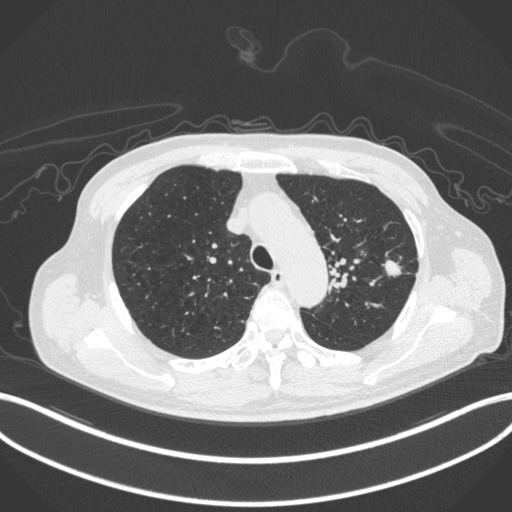
Chest CT, one axial slice; position 334 of 420 along the scan axis; reconstruction kernel B31f; 120 kVp; lung window (W 1500 / L -600 HU); 1 mm slice thickness; 512 × 512 image matrix, field of view 400 × 400 mm. Patient: male, 77 years. From the clinical record (not read from this slice): clinical TNM (as recorded): T3 N1 M0.
Structures marked on this image (bounding box drawn by a radiologist):
- lung tumour (recorded histology: adenocarcinoma): bounding box (x1, y1, x2, y2) in pixels: (383, 258, 404, 278)